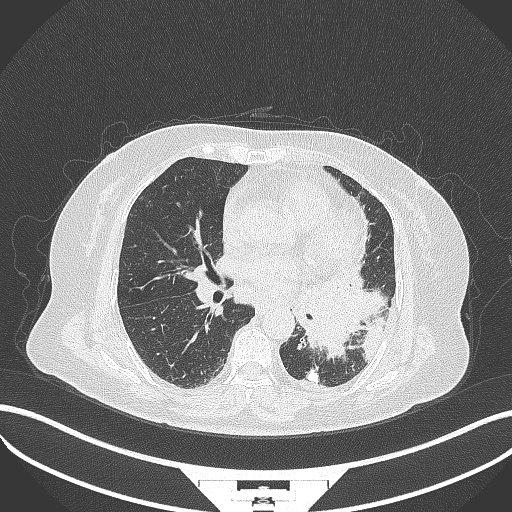
Chest CT, one axial slice; slice 170 of 322 in the series (ordered by position); lung window (W 1500 / L -600 HU); 1 mm slice thickness; 512 × 512 image matrix. Female patient, age 69 years. From the clinical record (not read from this slice): clinical TNM (as recorded): T2b N3 M1.
Structures marked on this image (rectangle marked by the reading radiologist):
- lung tumour (recorded histology: adenocarcinoma): box from (x=294, y=257) to (x=389, y=360) px